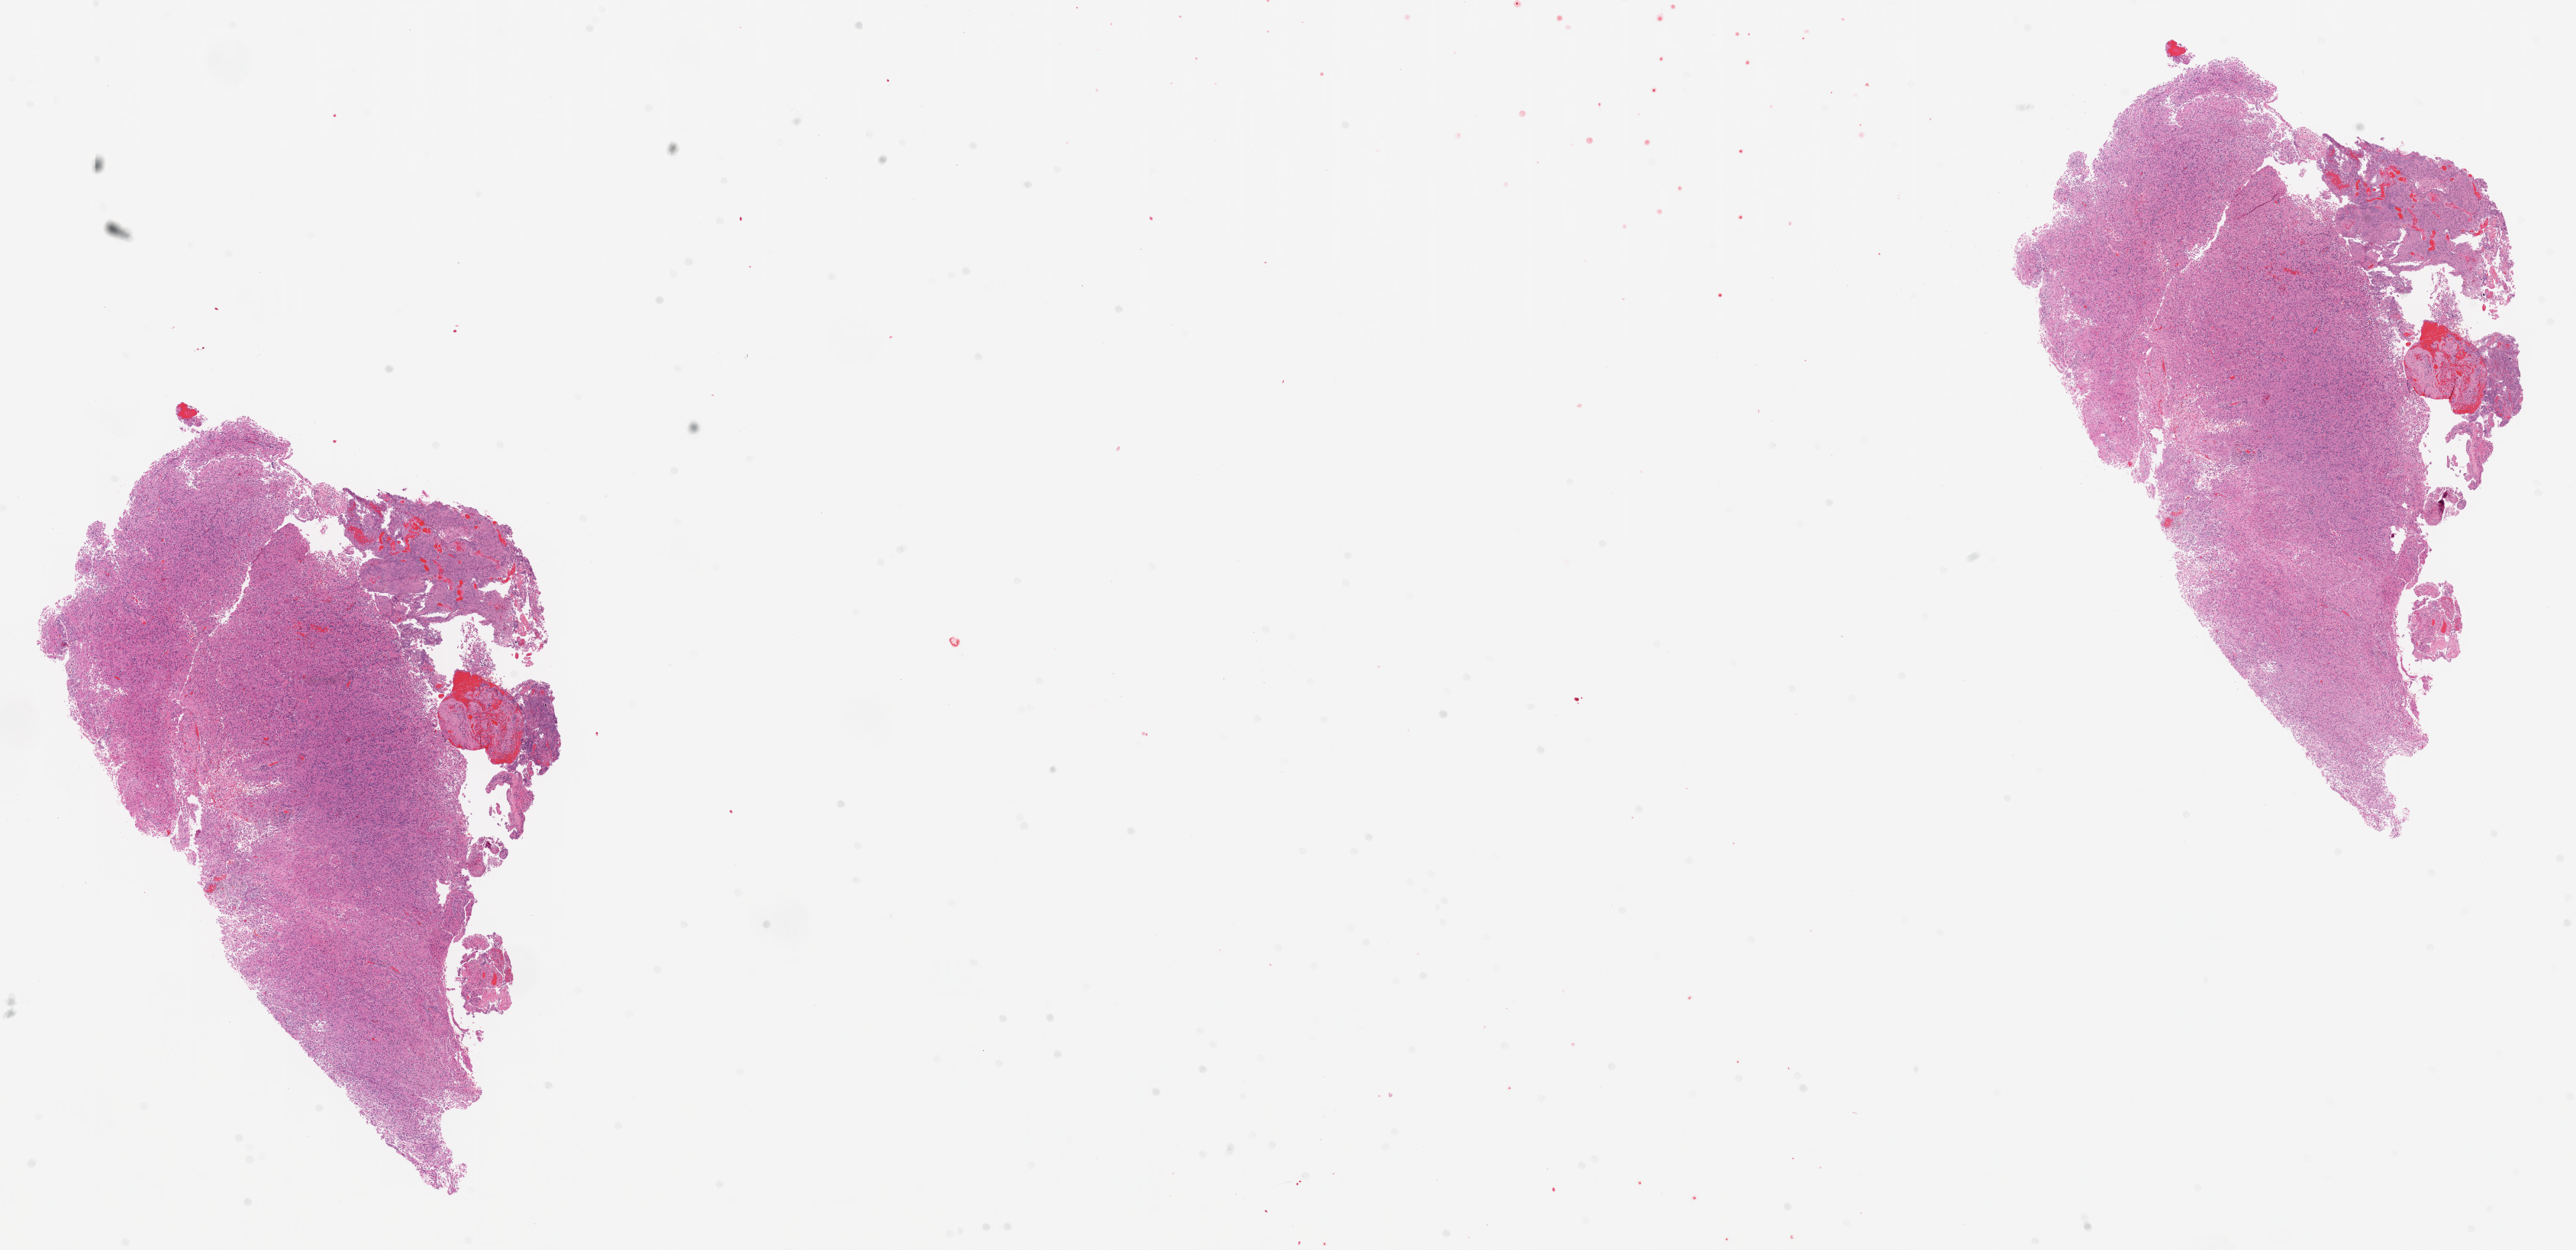
Digitized H&E tissue section (whole slide), shown as a low-resolution overview of the whole scanned area (about 27.1 x 13.1 mm); frozen section from the top of the tissue portion; sample: primary tumour, brain. Patient: male, age at initial diagnosis 72 years. Composition of this section per pathologist review: tumour cells 100%, tumour nuclei 75%, normal cells 0%, stromal cells 0%, necrosis 0%.
Pathologic diagnosis: Glioblastoma.